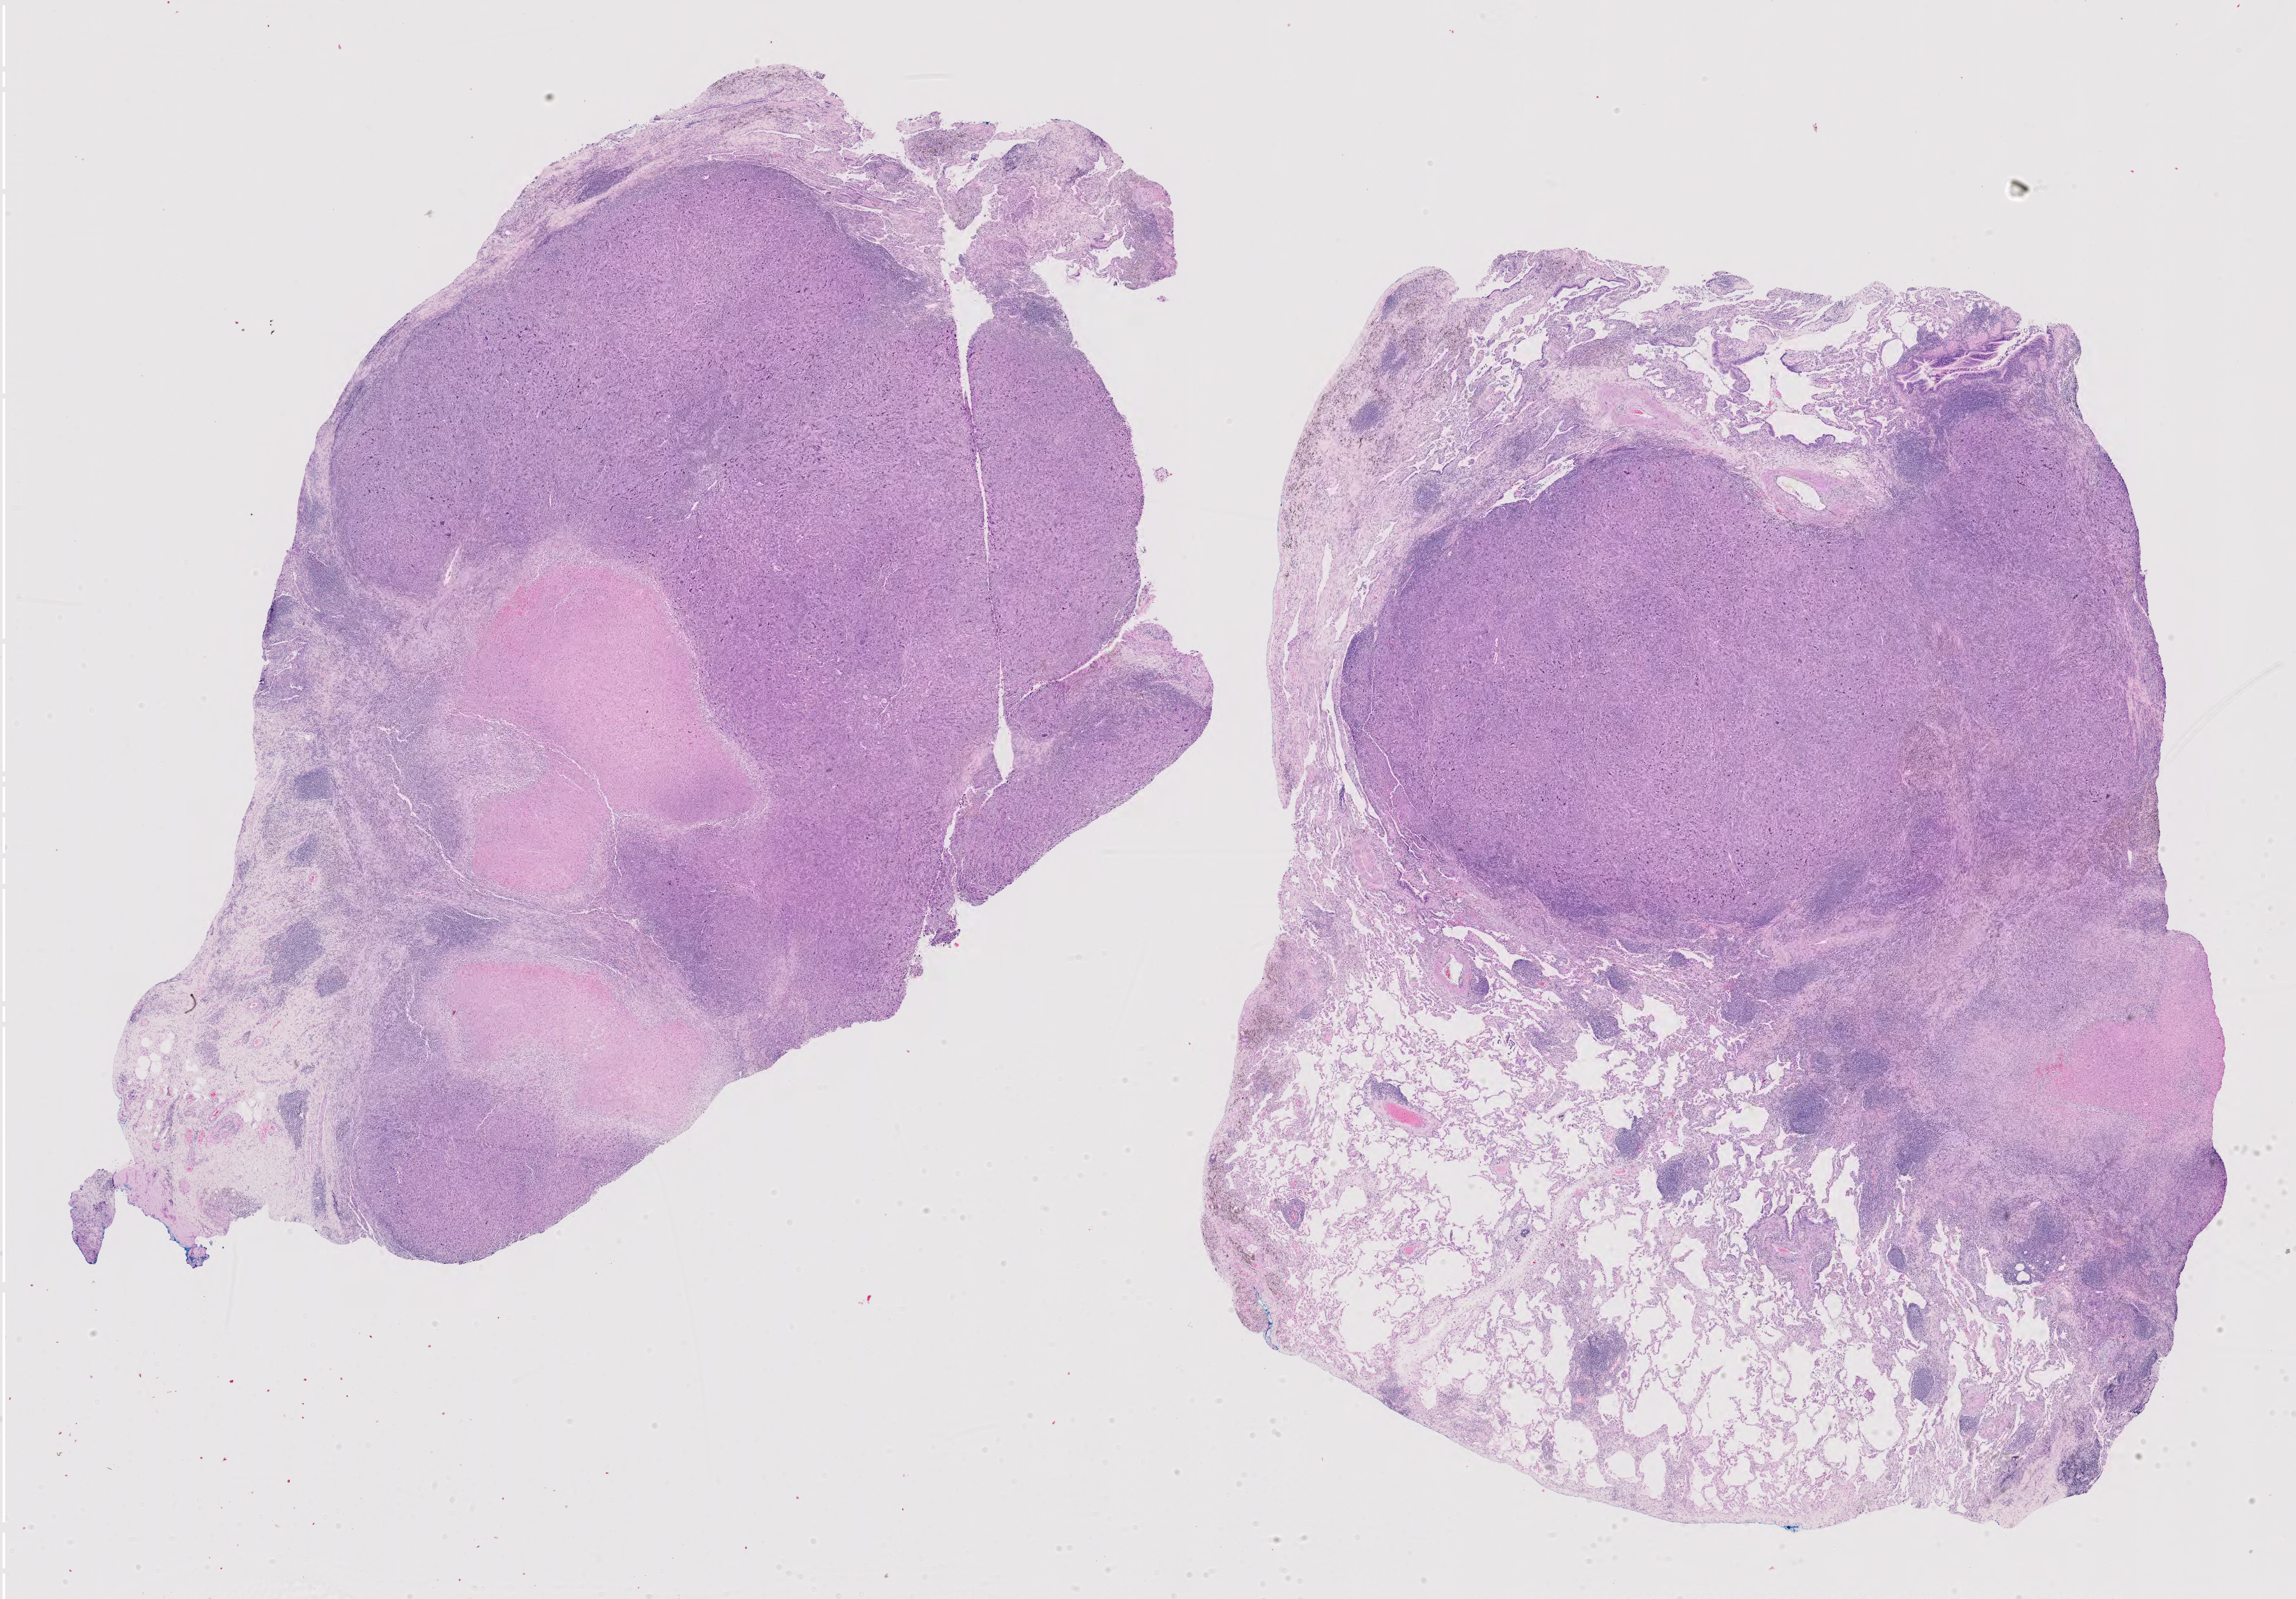
H&E-stained whole-slide image, a low-resolution overview of the entire scanned area, about 26.1 x 18.1 mm; formalin-fixed paraffin-embedded (FFPE) diagnostic section; primary tumour sample from the lung. Male patient; age at initial diagnosis 71 years.
- diagnosis: Adenocarcinoma, NOS (lower lobe, lung)
- laterality: left
- AJCC pathologic stage: IA (7th edition)